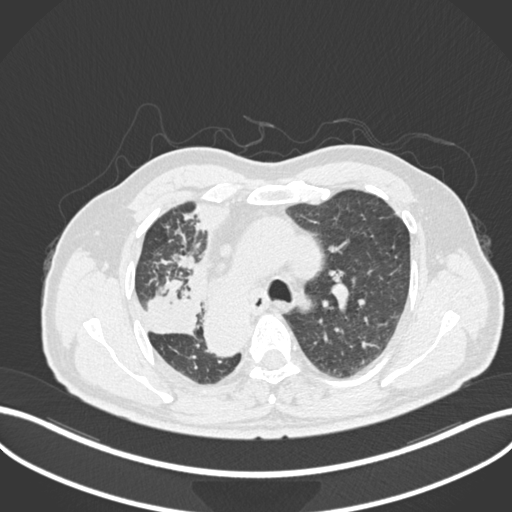
Chest CT, one axial slice; position 167 of 206 along the scan axis; 120 kVp; lung window (W 1500 / L -600 HU); 1 mm slice thickness; 512 × 512 image matrix. Patient: male, 67 years. From the clinical record (not read from this slice): clinical TNM (as recorded): T2a N0 M0.
Annotated regions visible in this slice (rectangle marked by the reading radiologist):
- lung tumour (recorded histology: squamous cell carcinoma): bounding box <141,275,202,338> (left, top, right, bottom; pixels)